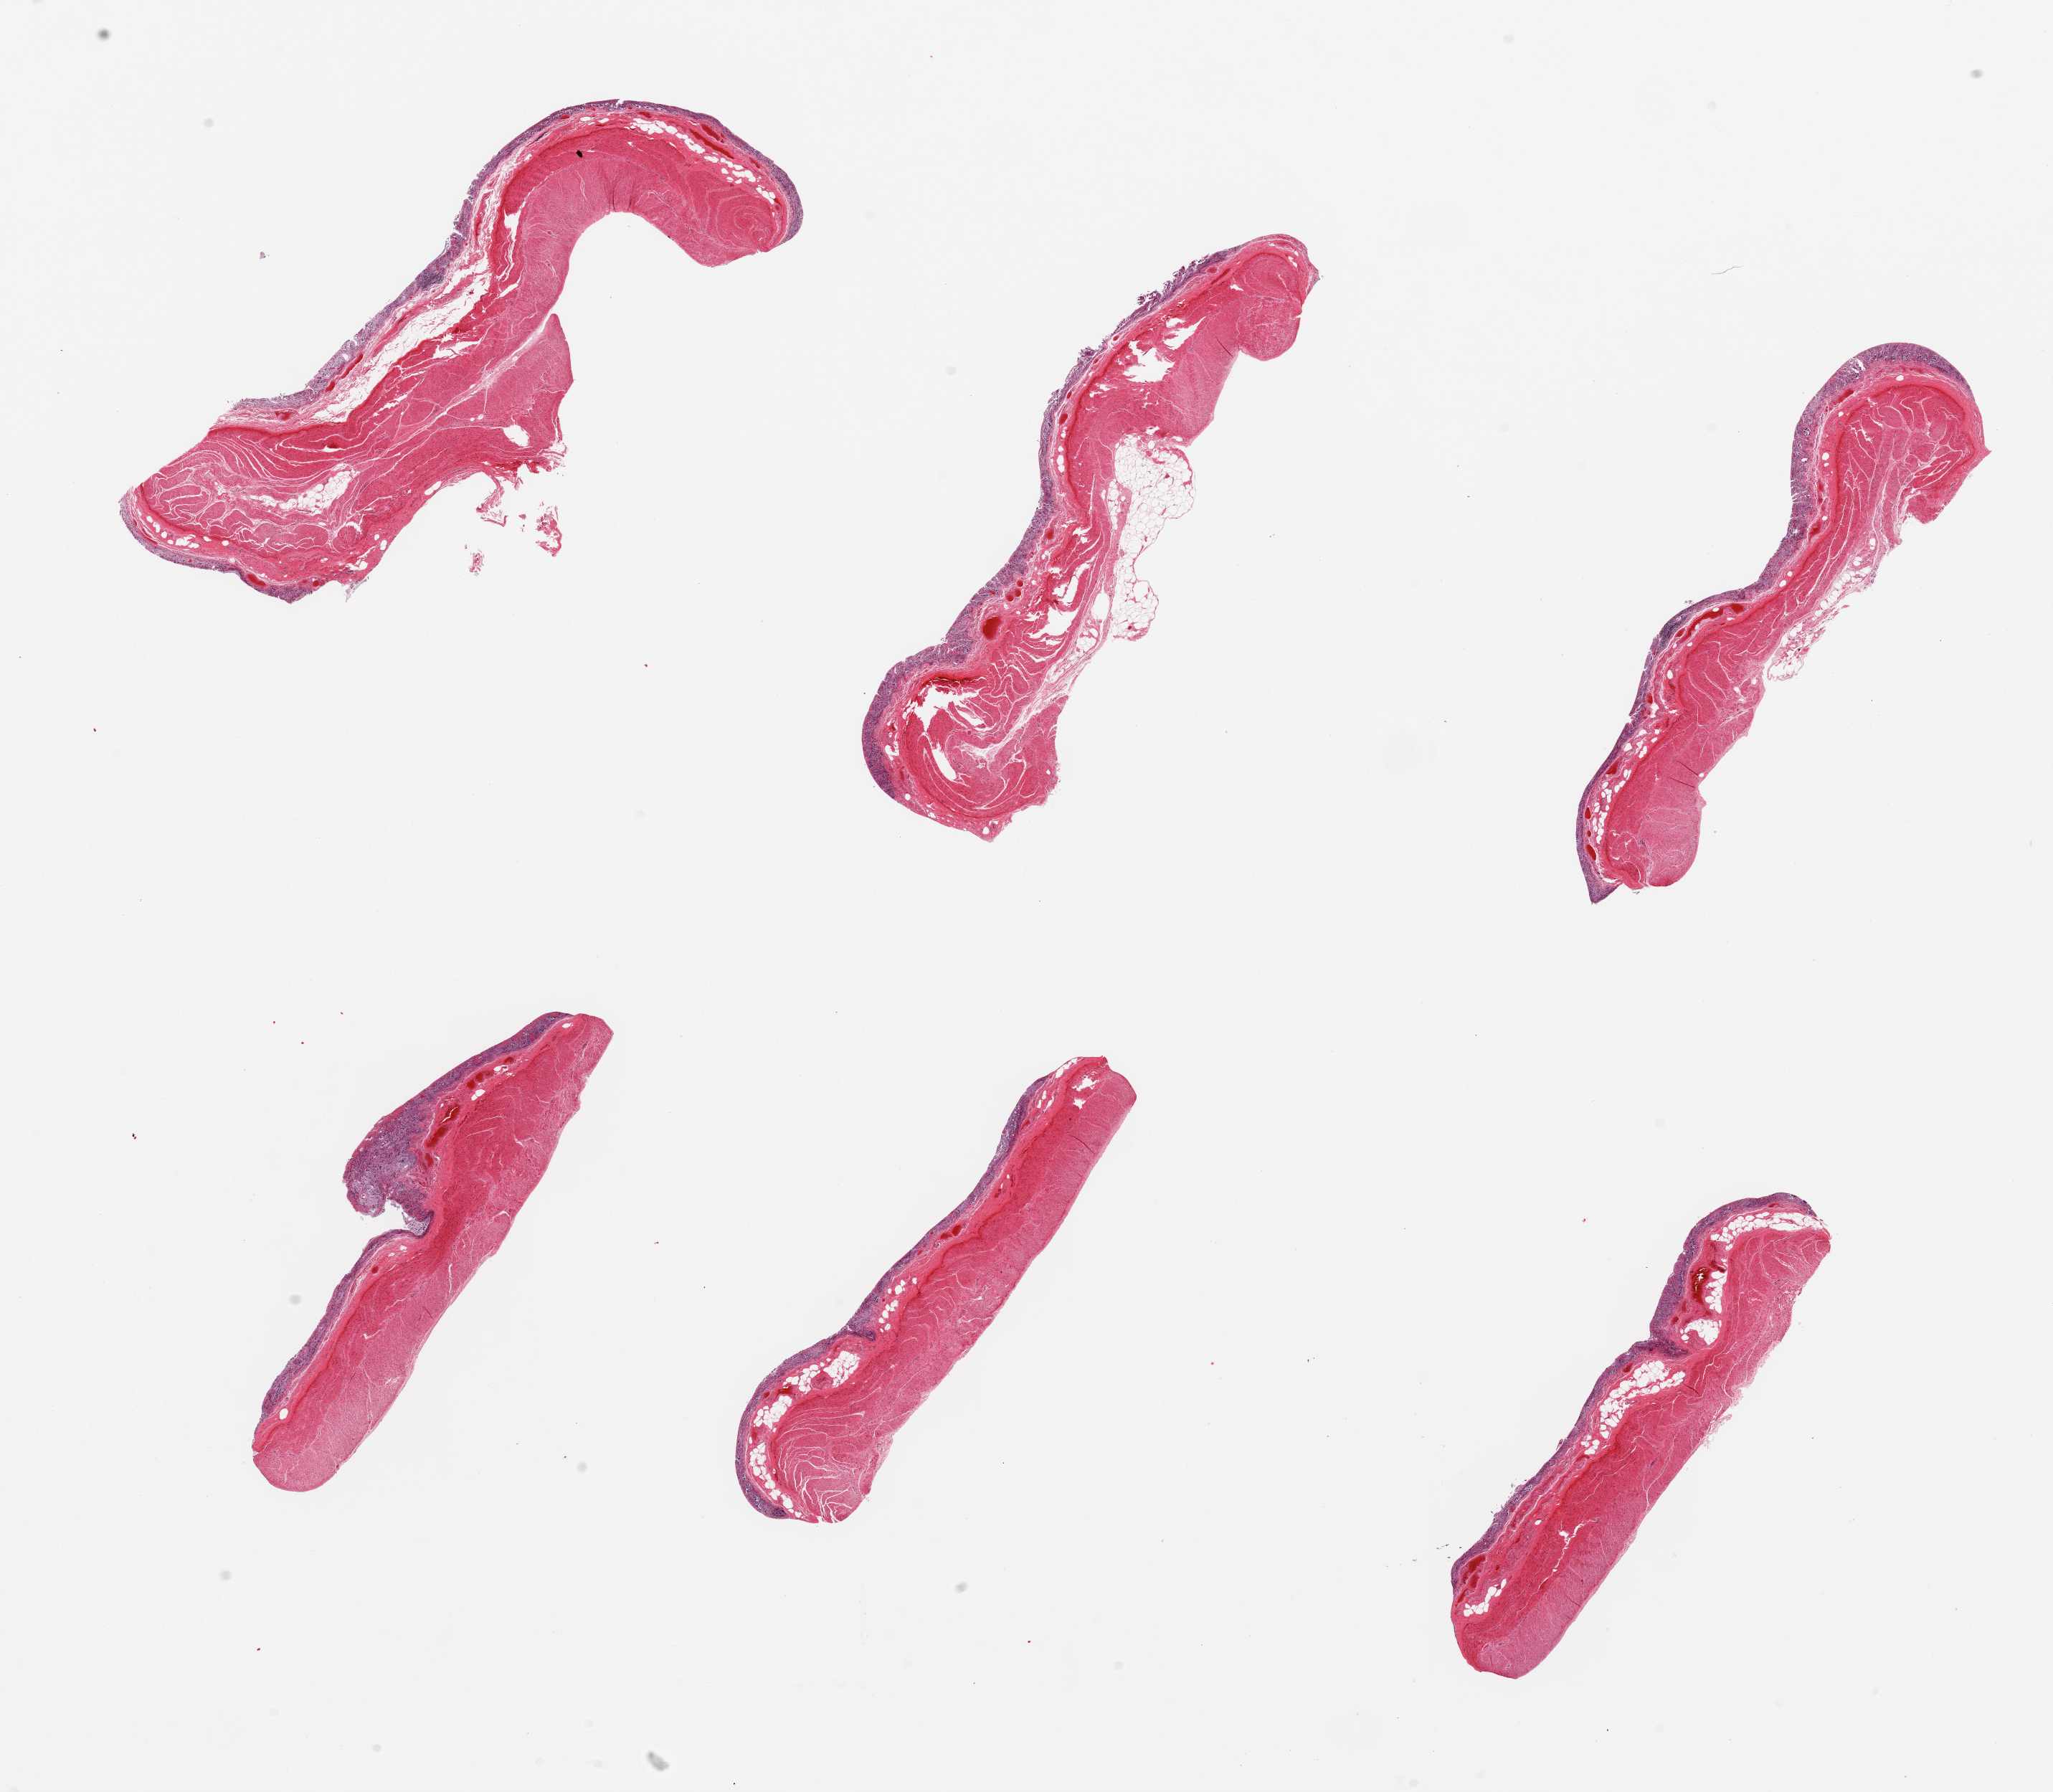
Digitized haematoxylin and eosin-stained section, whole scanned area (about 22.6 x 19.8 mm) shown as a low-resolution overview. PAXgene-fixed, paraffin-embedded tissue. Section of transverse colon (target tissue). Donor tissue sample.
- reviewer comment on this tissue sample: 6 pieces; mucosa autolyzed; muscle intact